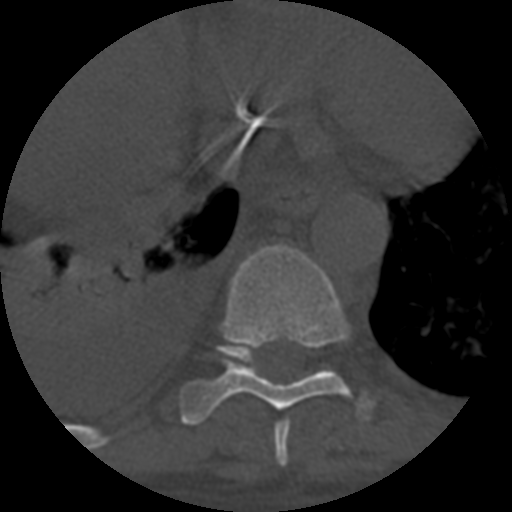
CT including the spine, one axial slice. Reconstruction kernel STANDARD. 120 kVp. One of 3 acquisitions stored at this slice position. Bone window (W 1800 / L 400 HU). 1.25 mm slice thickness. 512 × 512 image matrix, field of view 160 × 160 mm. Patient age 55 years. Case-level facts recorded for this patient, not image findings: primary cancer: colon; vertebrae with lytic lesions (as recorded): T12, L1, L5.
Annotated regions visible in this slice (semi-automatic segmentation, software-assisted and operator-edited):
- T10 vertebra: box from (x=221, y=343) to (x=253, y=362) px
- T8 vertebra: (x=274, y=419)–(x=290, y=467)
- T9 vertebra: (x=181, y=243)–(x=373, y=425)